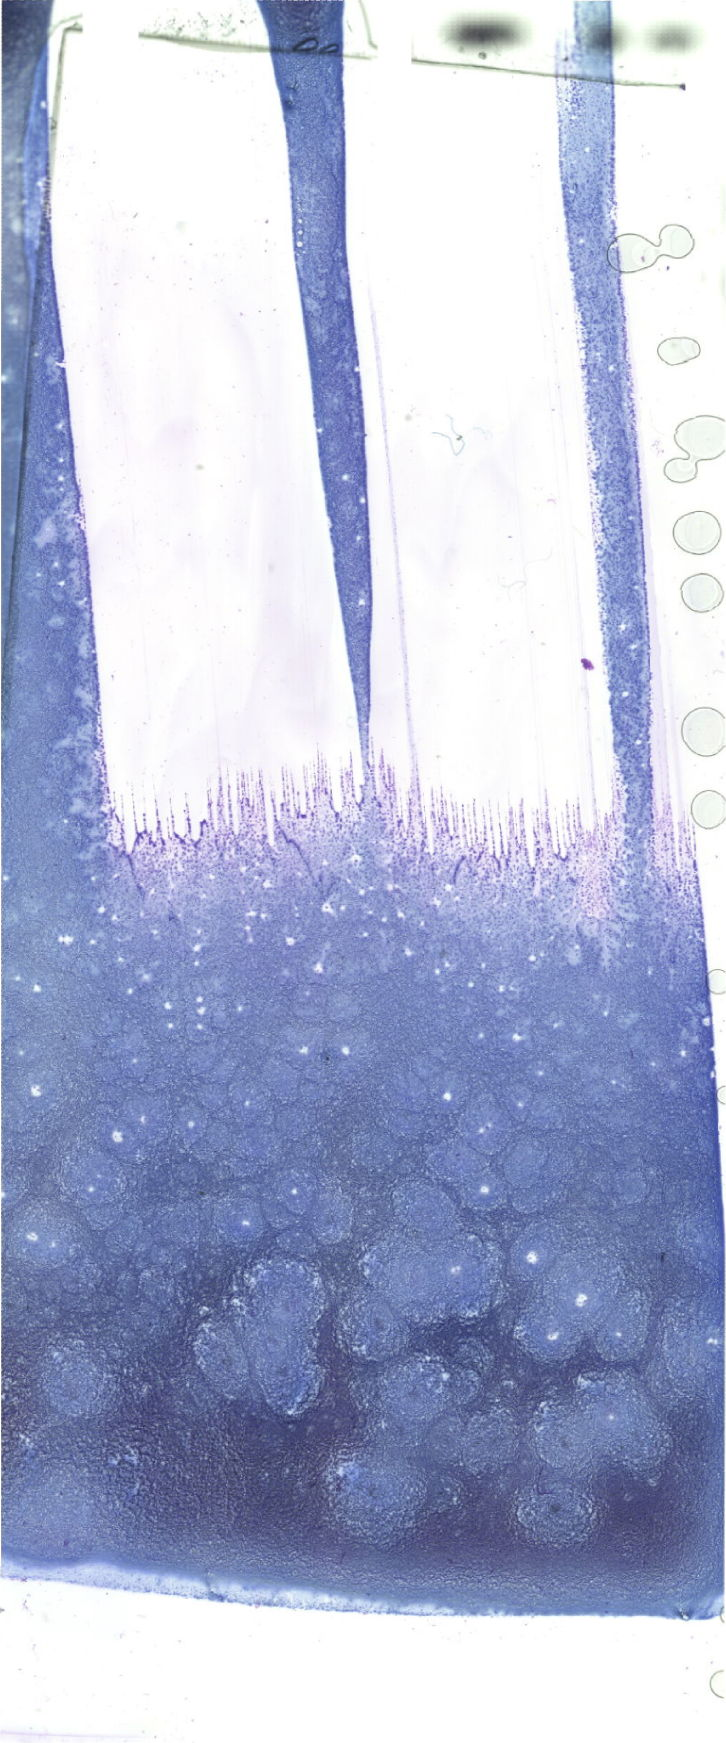
May-Grünwald–Giemsa-stained marrow aspirate smear (whole slide) — whole scanned area (about 20.6 x 49.4 mm) shown as a low-resolution overview. Female patient.
Diagnosis: Acute Promyelocytic Leukemia with t(15;17)(q24.1;q21.2);PML-RARA.